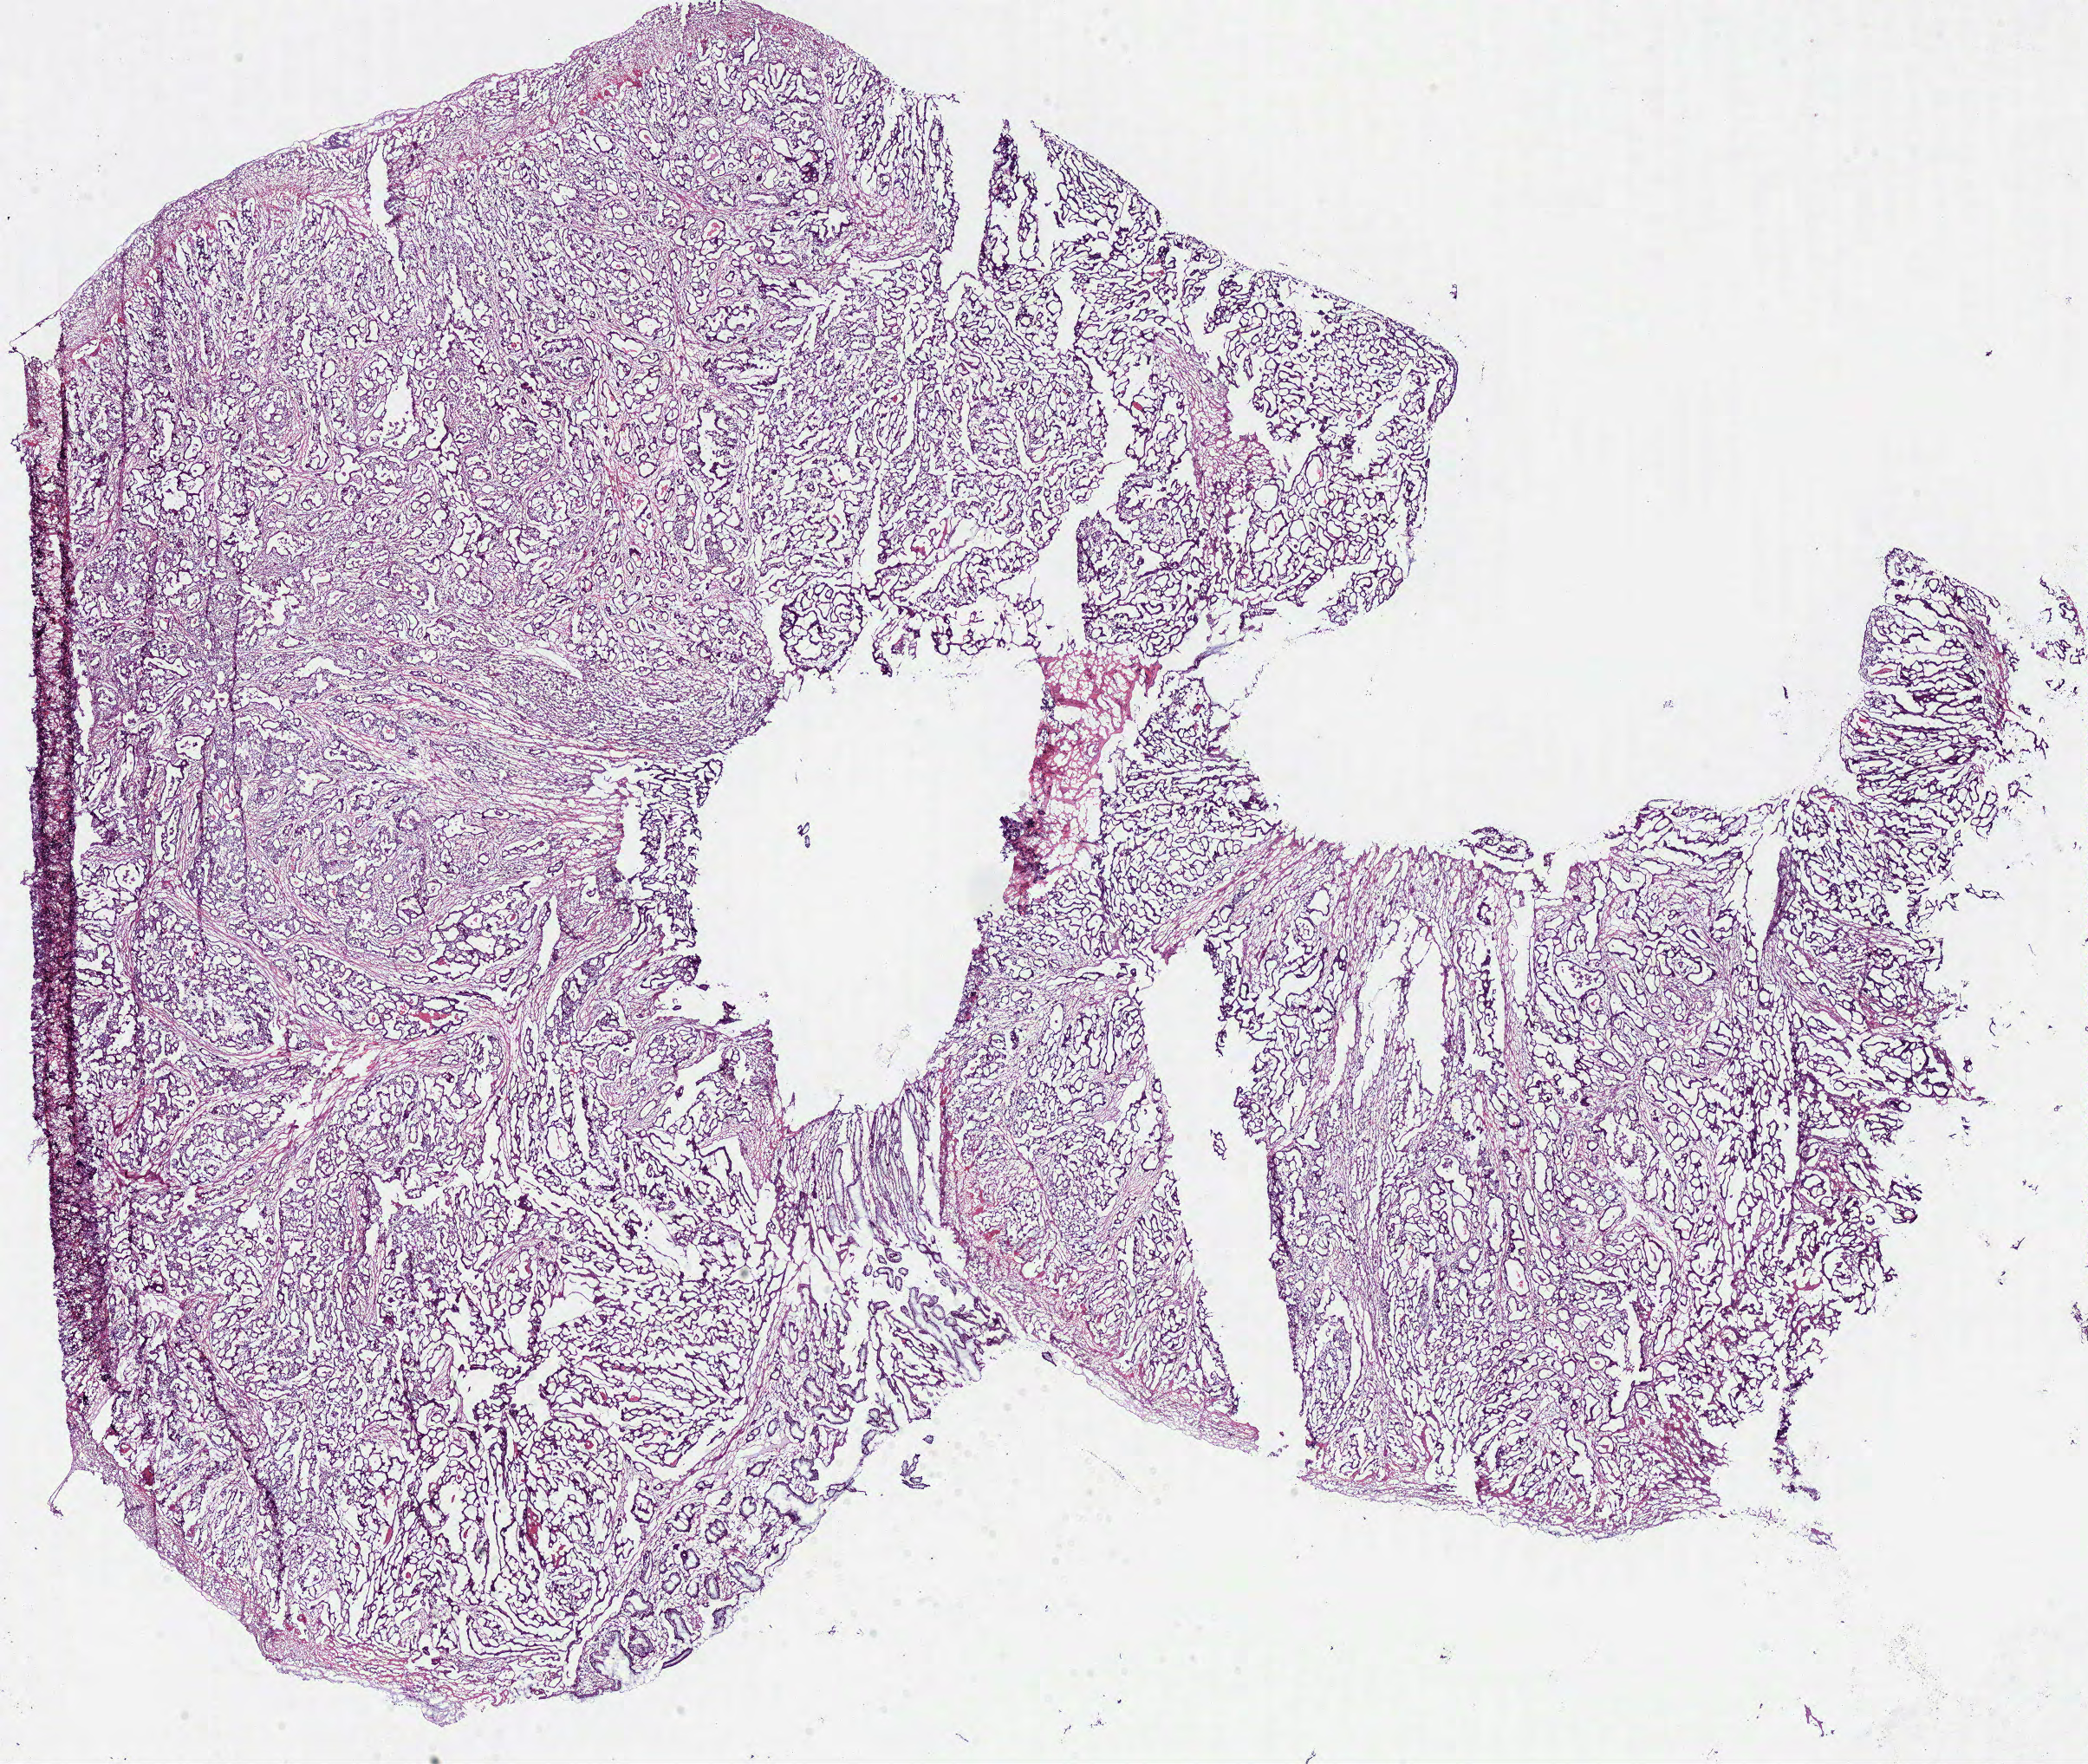
Whole-slide histology image, H&E — a low-resolution overview of the entire scanned area, about 19.0 x 16.0 mm (acquisition: 40x scan). Frozen section. Primary tumour sample from the colon. Female, age 54 years at initial diagnosis. Composition of this section per pathologist review: tumour cells 90%, tumour nuclei 80%, normal cells 0%, stromal cells 5%, necrosis 5%.
AJCC pathologic stage: I (7th edition). TNM: T1 N0 M0. Pathologic diagnosis: Adenocarcinoma, NOS.